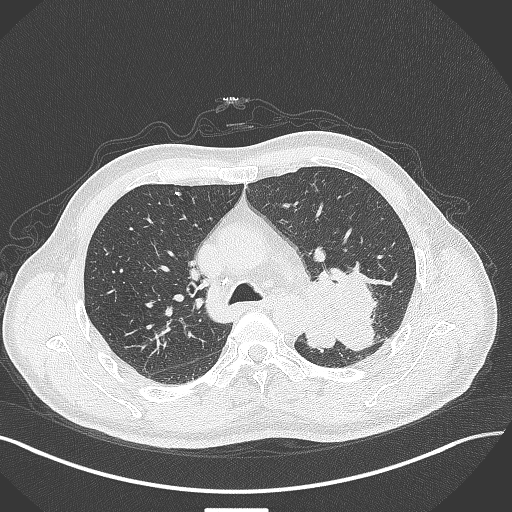
Chest CT, one axial slice. Position 285 of 429 along the scan axis. Reconstruction kernel B70f. 120 kVp. Lung window (W 1500 / L -600 HU). 1 mm slice thickness. 512 × 512 image matrix. Male patient, age 55 years. From the clinical record (not read from this slice): clinical TNM (as recorded): T3 N0 M1c; histopathological grade: G3.
Outlined on this slice (rectangle marked by the reading radiologist):
- lung tumour (recorded histology: adenocarcinoma): box from (x=308, y=265) to (x=391, y=352) px